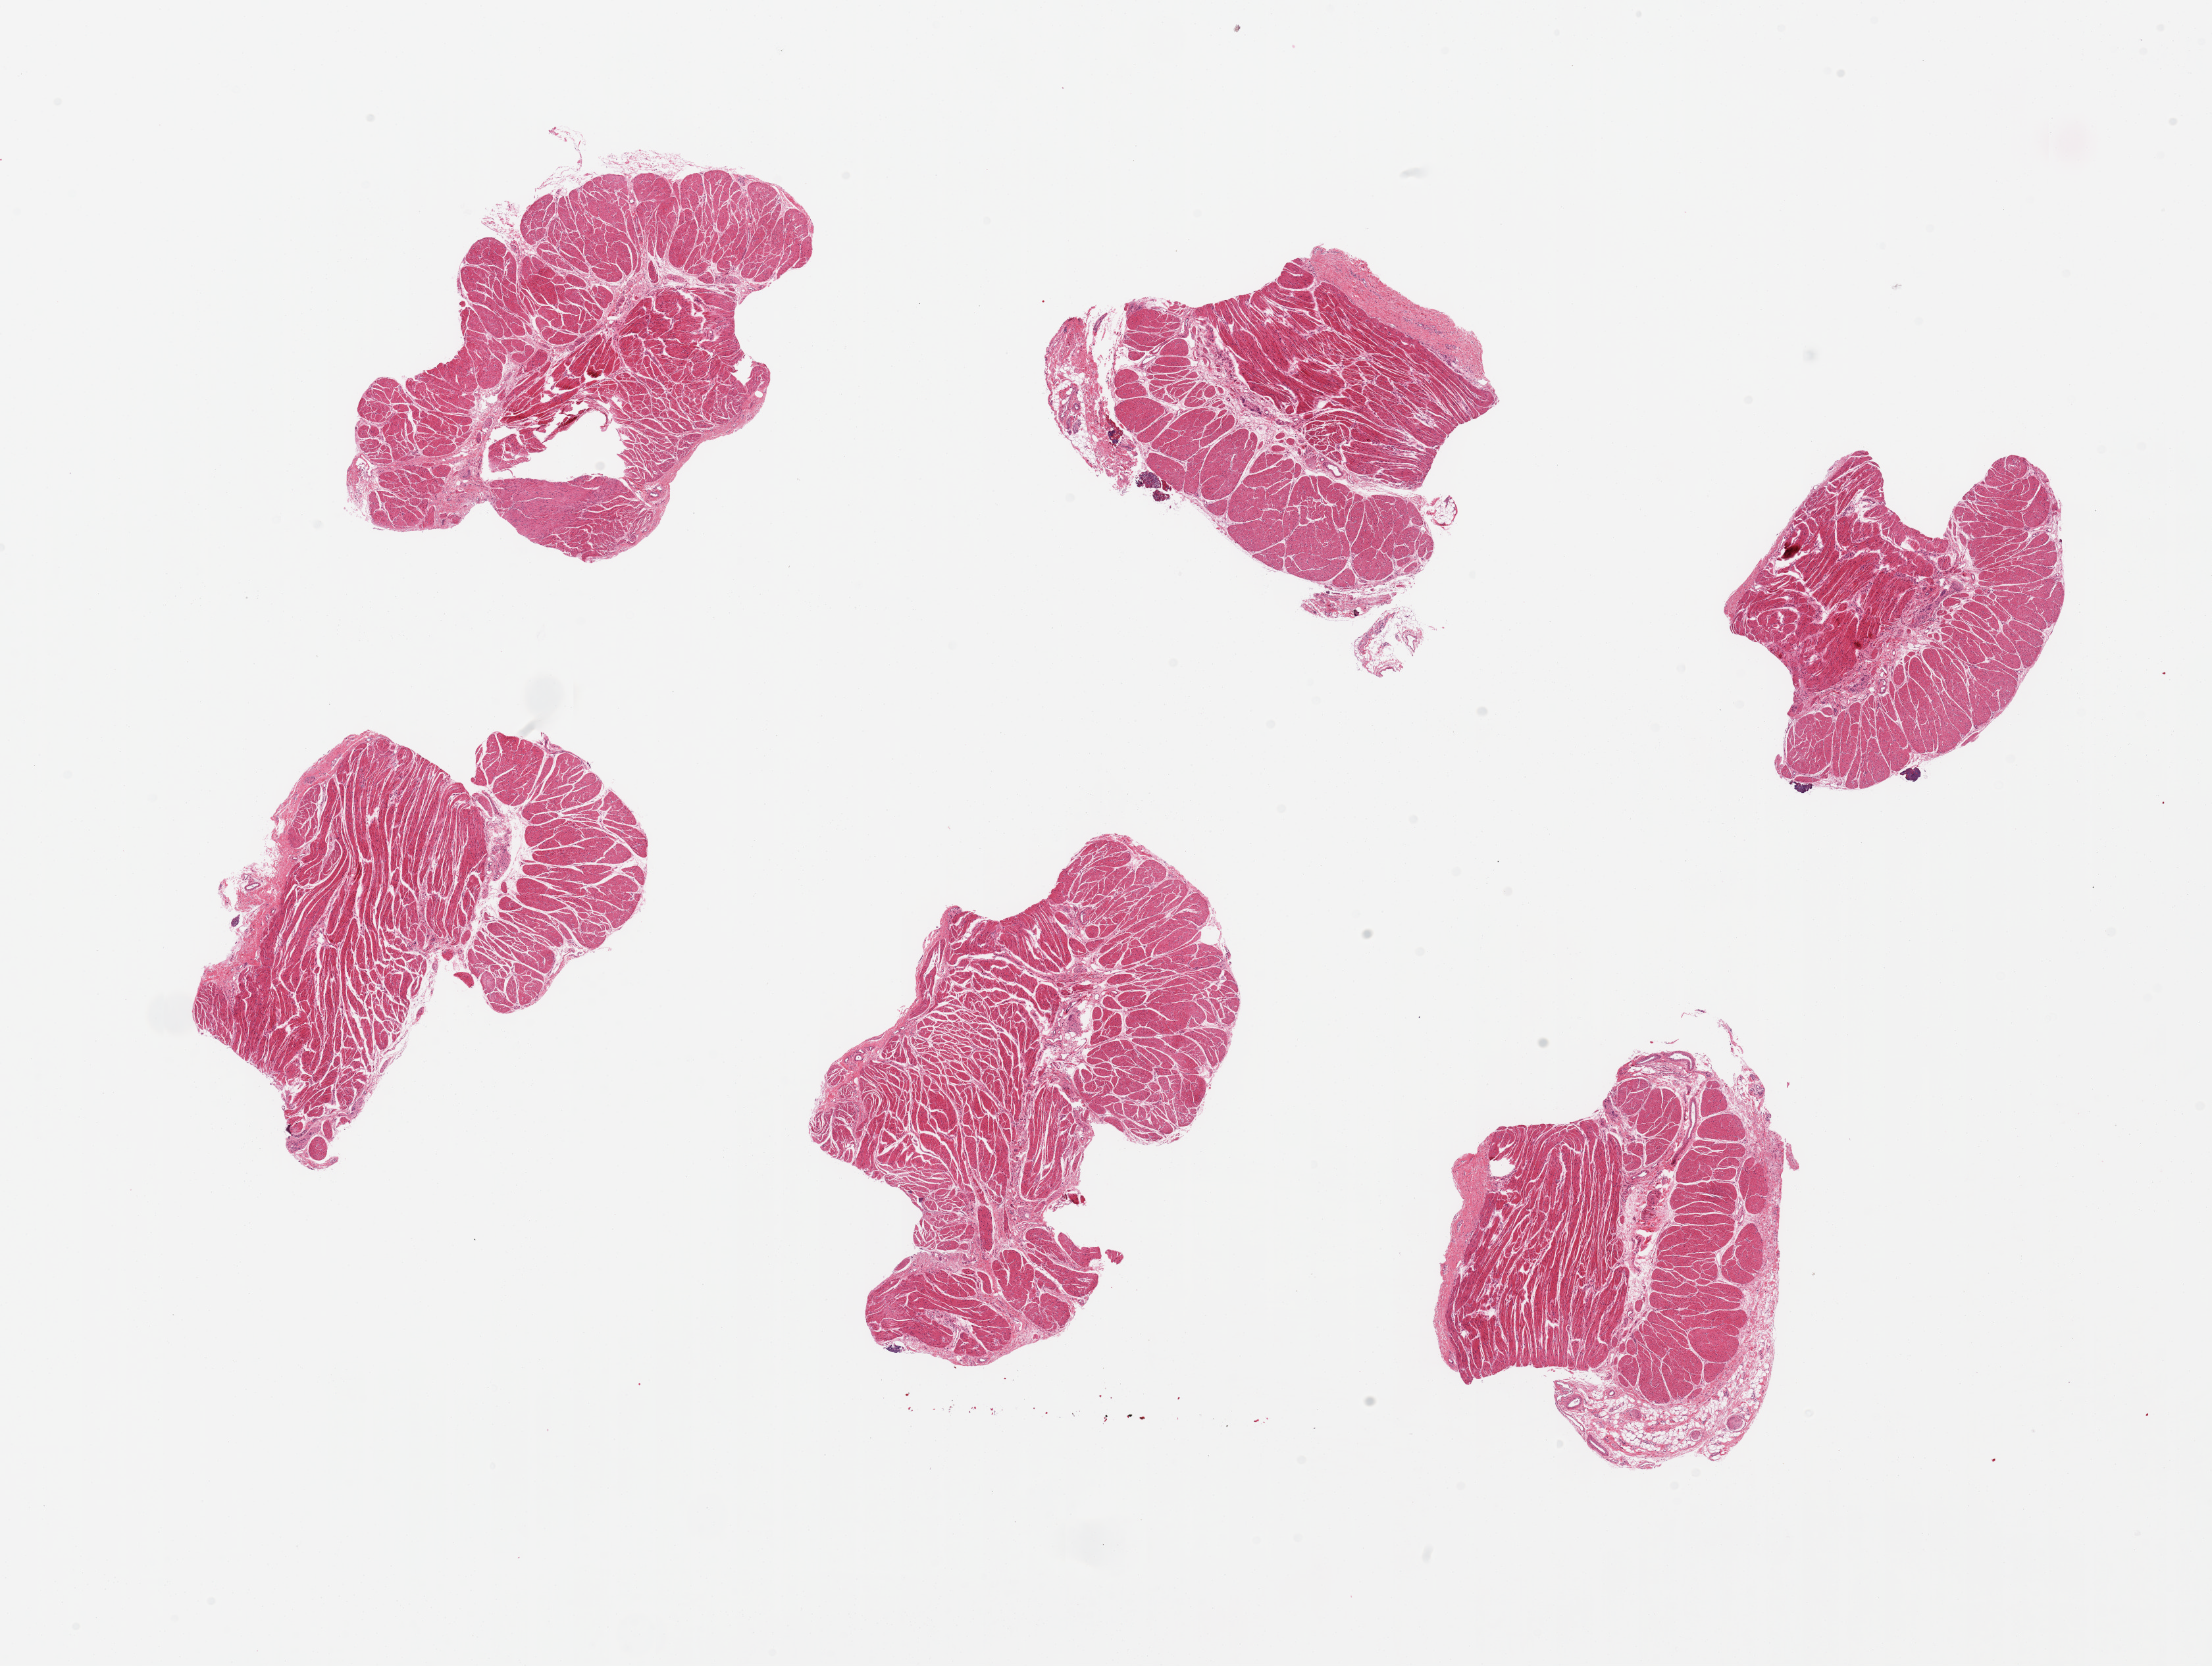
Digitized hematoxylin and eosin (H&E)-stained section, brightfield — a low-resolution overview of the entire scanned area, about 26.6 x 20.0 mm (acquisition: 20x scan). PAXgene-fixed, paraffin-embedded tissue. Section of gastroesophageal junction (target tissue). Tissue donor sample.
Pathologist's review note for this sample: 6 pieces, well trimmed, few detached fragments of squamous epithelium.